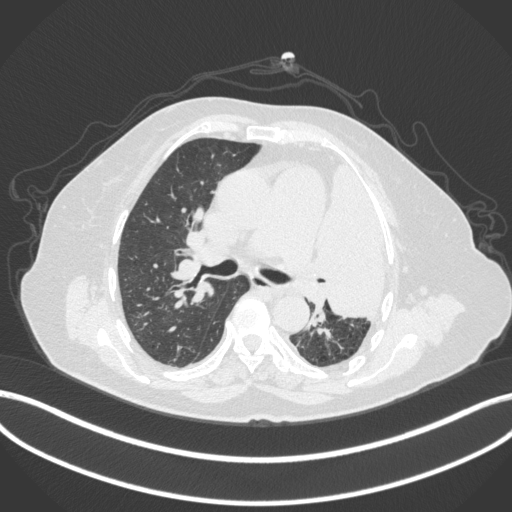
Chest CT, one axial slice; position 239 of 399 along the scan axis; reconstruction kernel B31f; 120 kVp; lung window (W 1500 / L -600 HU); 1 mm slice thickness; 512 × 512 image matrix, field of view 400 × 400 mm. Female patient, age 75 years. From the clinical record (not read from this slice): clinical TNM (as recorded): T3 N3 M1.
Annotated regions visible in this slice (rectangle marked by the reading radiologist):
- lung tumour (recorded histology: adenocarcinoma): bounding box [x1, y1, x2, y2] px = [312, 146, 410, 328]